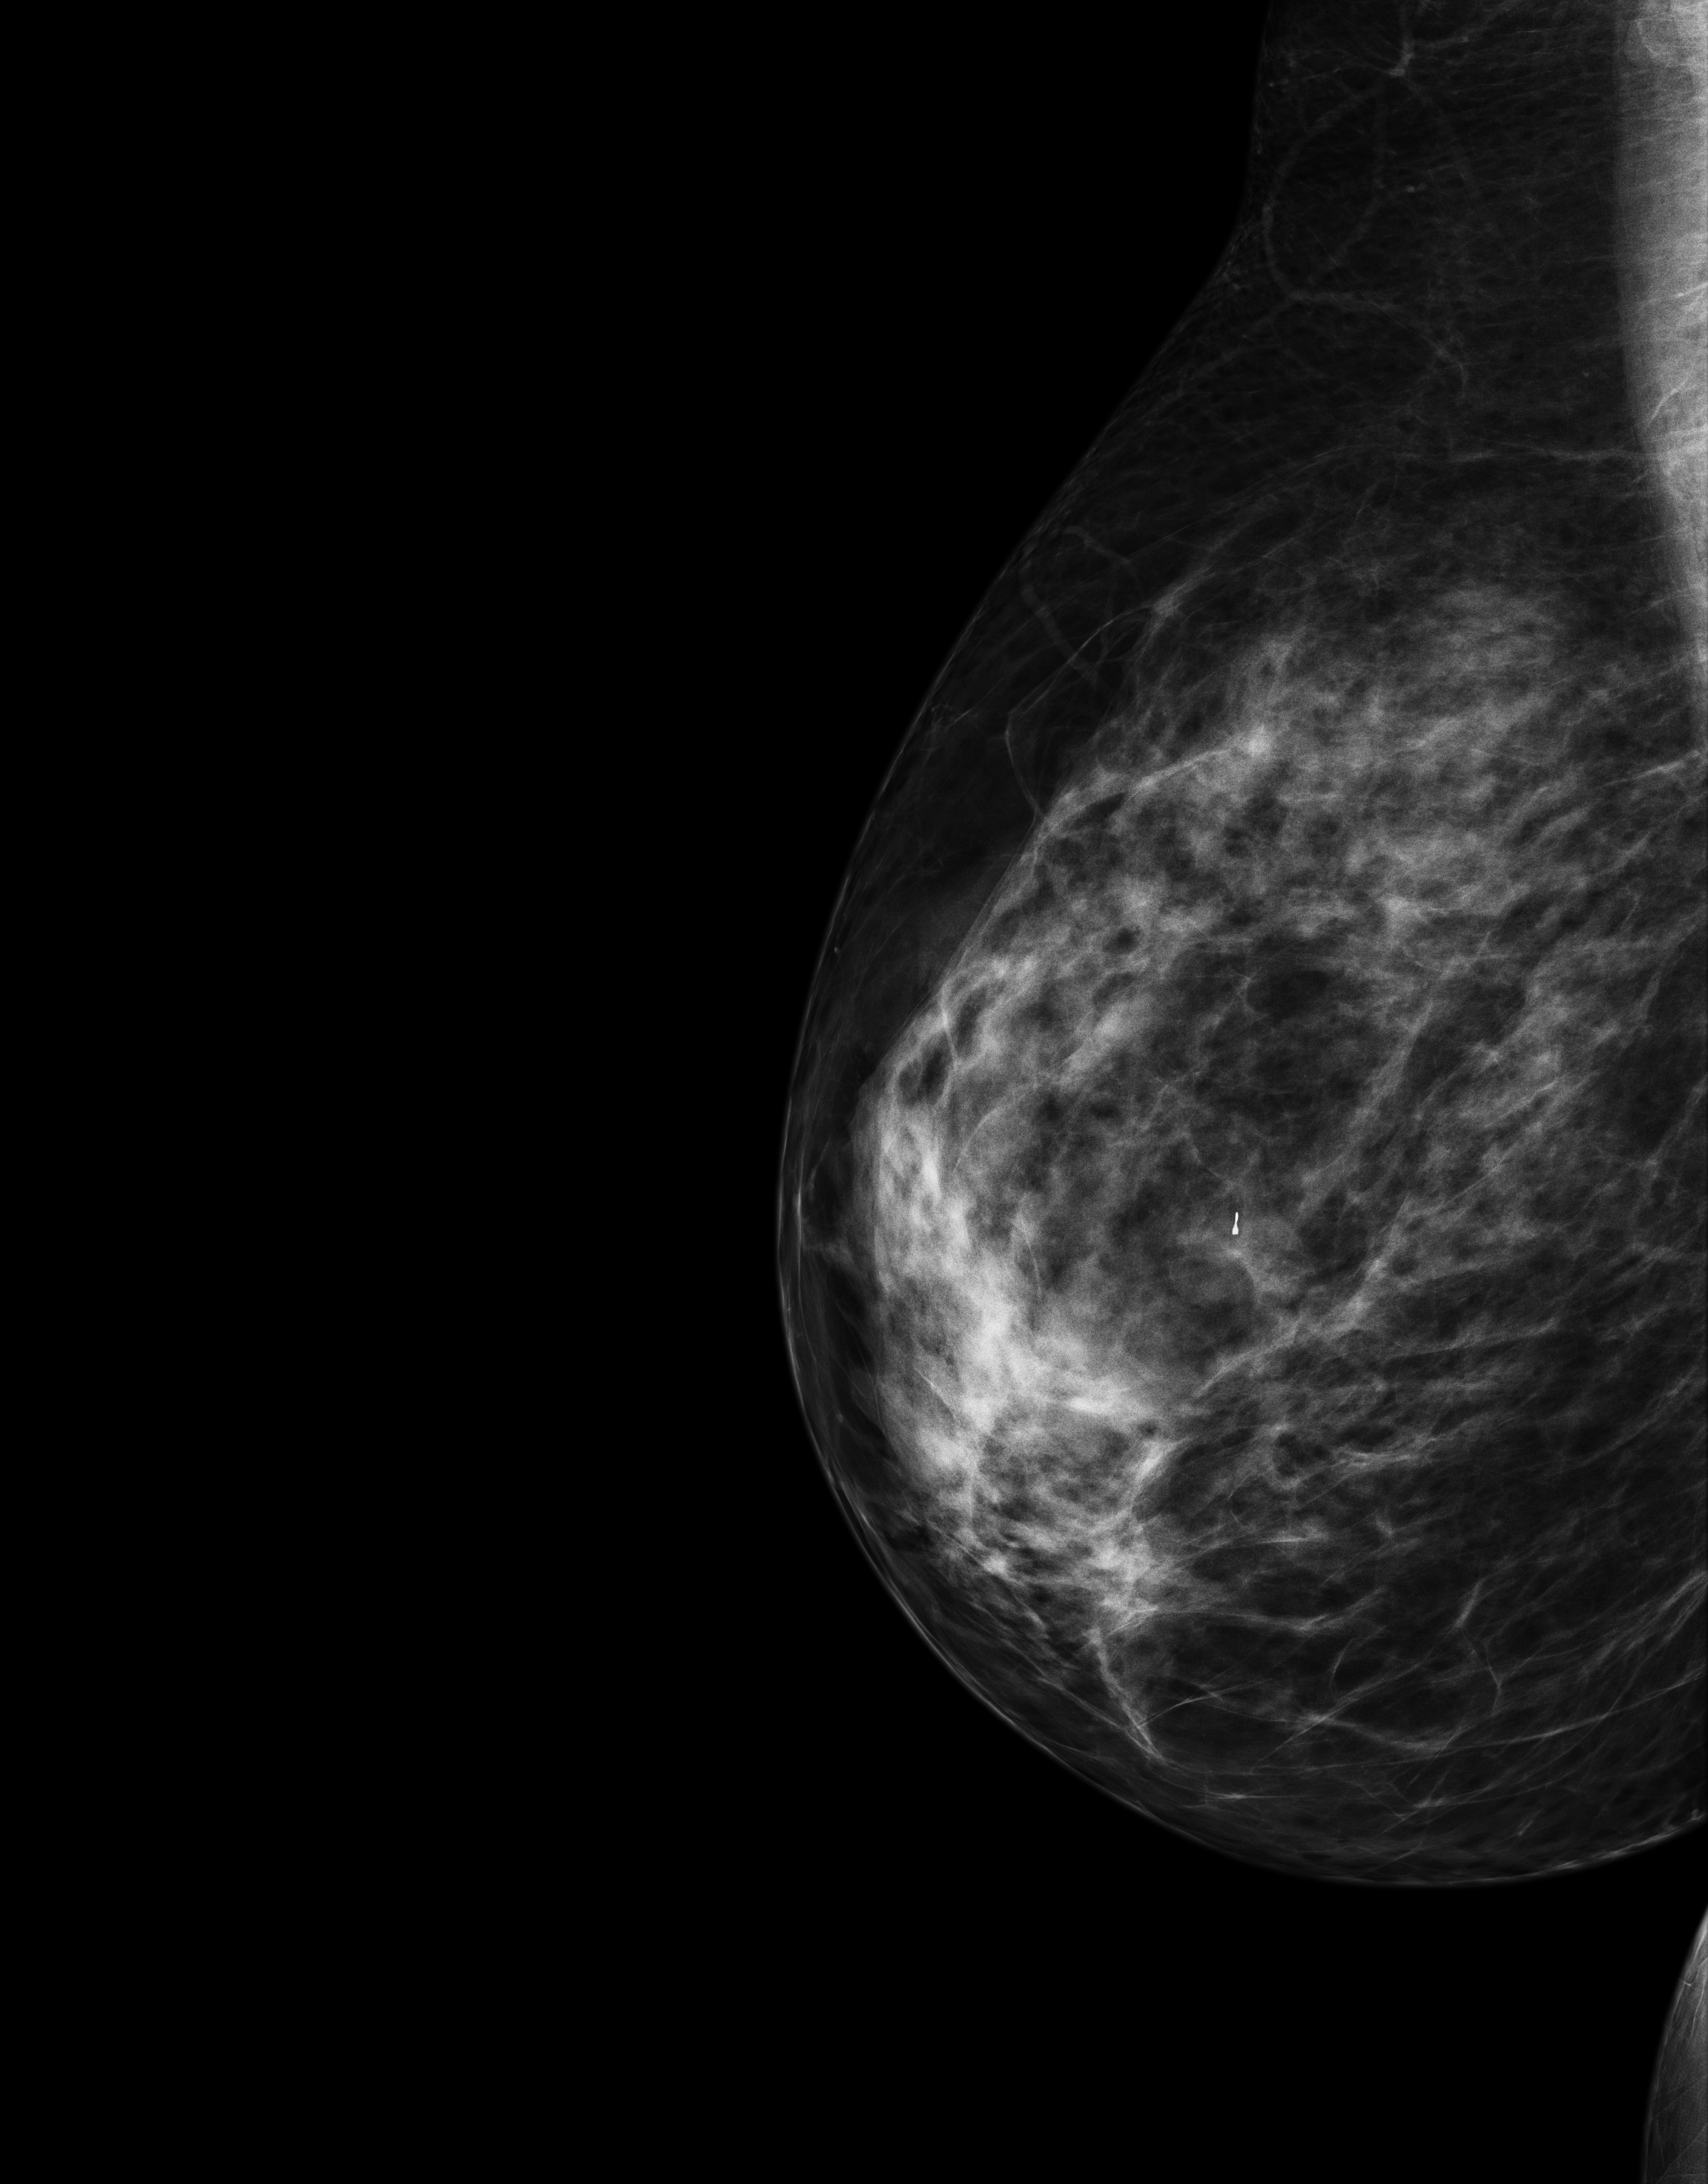
Annual screening mammography examination; compressed breast thickness 82 mm; system: Senographe Essential ADS_56.21.3. Patient: female, 43 years.
Image type: full-field digital mammogram. Breast: right. Projection: laterally exaggerated craniocaudal (XCCL) view.